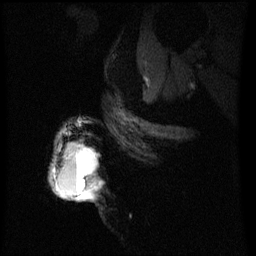
Breast MRI (dynamic contrast-enhanced), one sagittal slice. Dynamic contrast-enhanced series, image 2 of 3 at this slice position (ordered by acquisition). 1.5 T. TE 4.2 ms, TR 8 ms. 256 × 256 image matrix. Female patient, age 50 years.
Structures marked on this image (semi-automatic segmentation, software-assisted and operator-edited):
- analysis volume of interest (the breast-tissue region the enhancement analysis was run in; not a lesion): bounding box (x1, y1, x2, y2) in pixels: (53, 146, 94, 201)
- tumour enhancement mask (voxels above the 70 % enhancement threshold inside the analysis volume of interest): (56, 150, 93, 201)